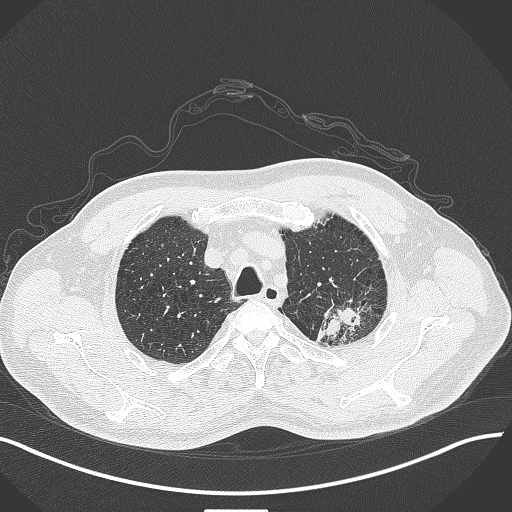
Chest CT, one axial slice. Position 352 of 429 along the scan axis. Lung window (W 1500 / L -600 HU). 1 mm slice thickness. 512 × 512 image matrix, field of view 400 × 400 mm. Male patient, age 55 years. Case-level facts recorded for this patient, not image findings: clinical TNM (as recorded): T3 N0 M1c; histopathological grade: G3.
Structures marked on this image (bounding box drawn by a radiologist):
- lung tumour (recorded histology: adenocarcinoma): bounding box <315,287,373,344> (left, top, right, bottom; pixels)